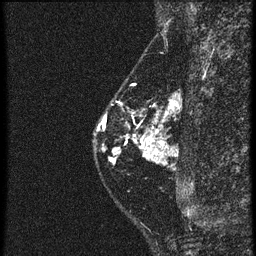
Breast MRI (dynamic contrast-enhanced), one sagittal slice. Slice 19 of 60 in the series (ordered by position). 4 images stored at this slice position (order not interpretable as contrast timing). 1.5 T. TE 4.2 ms, TR 20.4 ms. 1.5 mm slice thickness. 256 × 256 image matrix, field of view 180 × 180 mm. Female patient, age 46 years. From the clinical record (not read from this slice): setting: breast cancer imaged before/during neoadjuvant chemotherapy; receptor status: triple-negative.
Outlined on this slice (semi-automatically segmented with operator editing):
- analysis volume of interest (the breast-tissue region the enhancement analysis was run in; not a lesion): bounding box (x1, y1, x2, y2) in pixels: (92, 82, 165, 183)
- tumour enhancement mask (voxels above the 90 % enhancement threshold inside the analysis volume of interest): (104, 124, 155, 155)